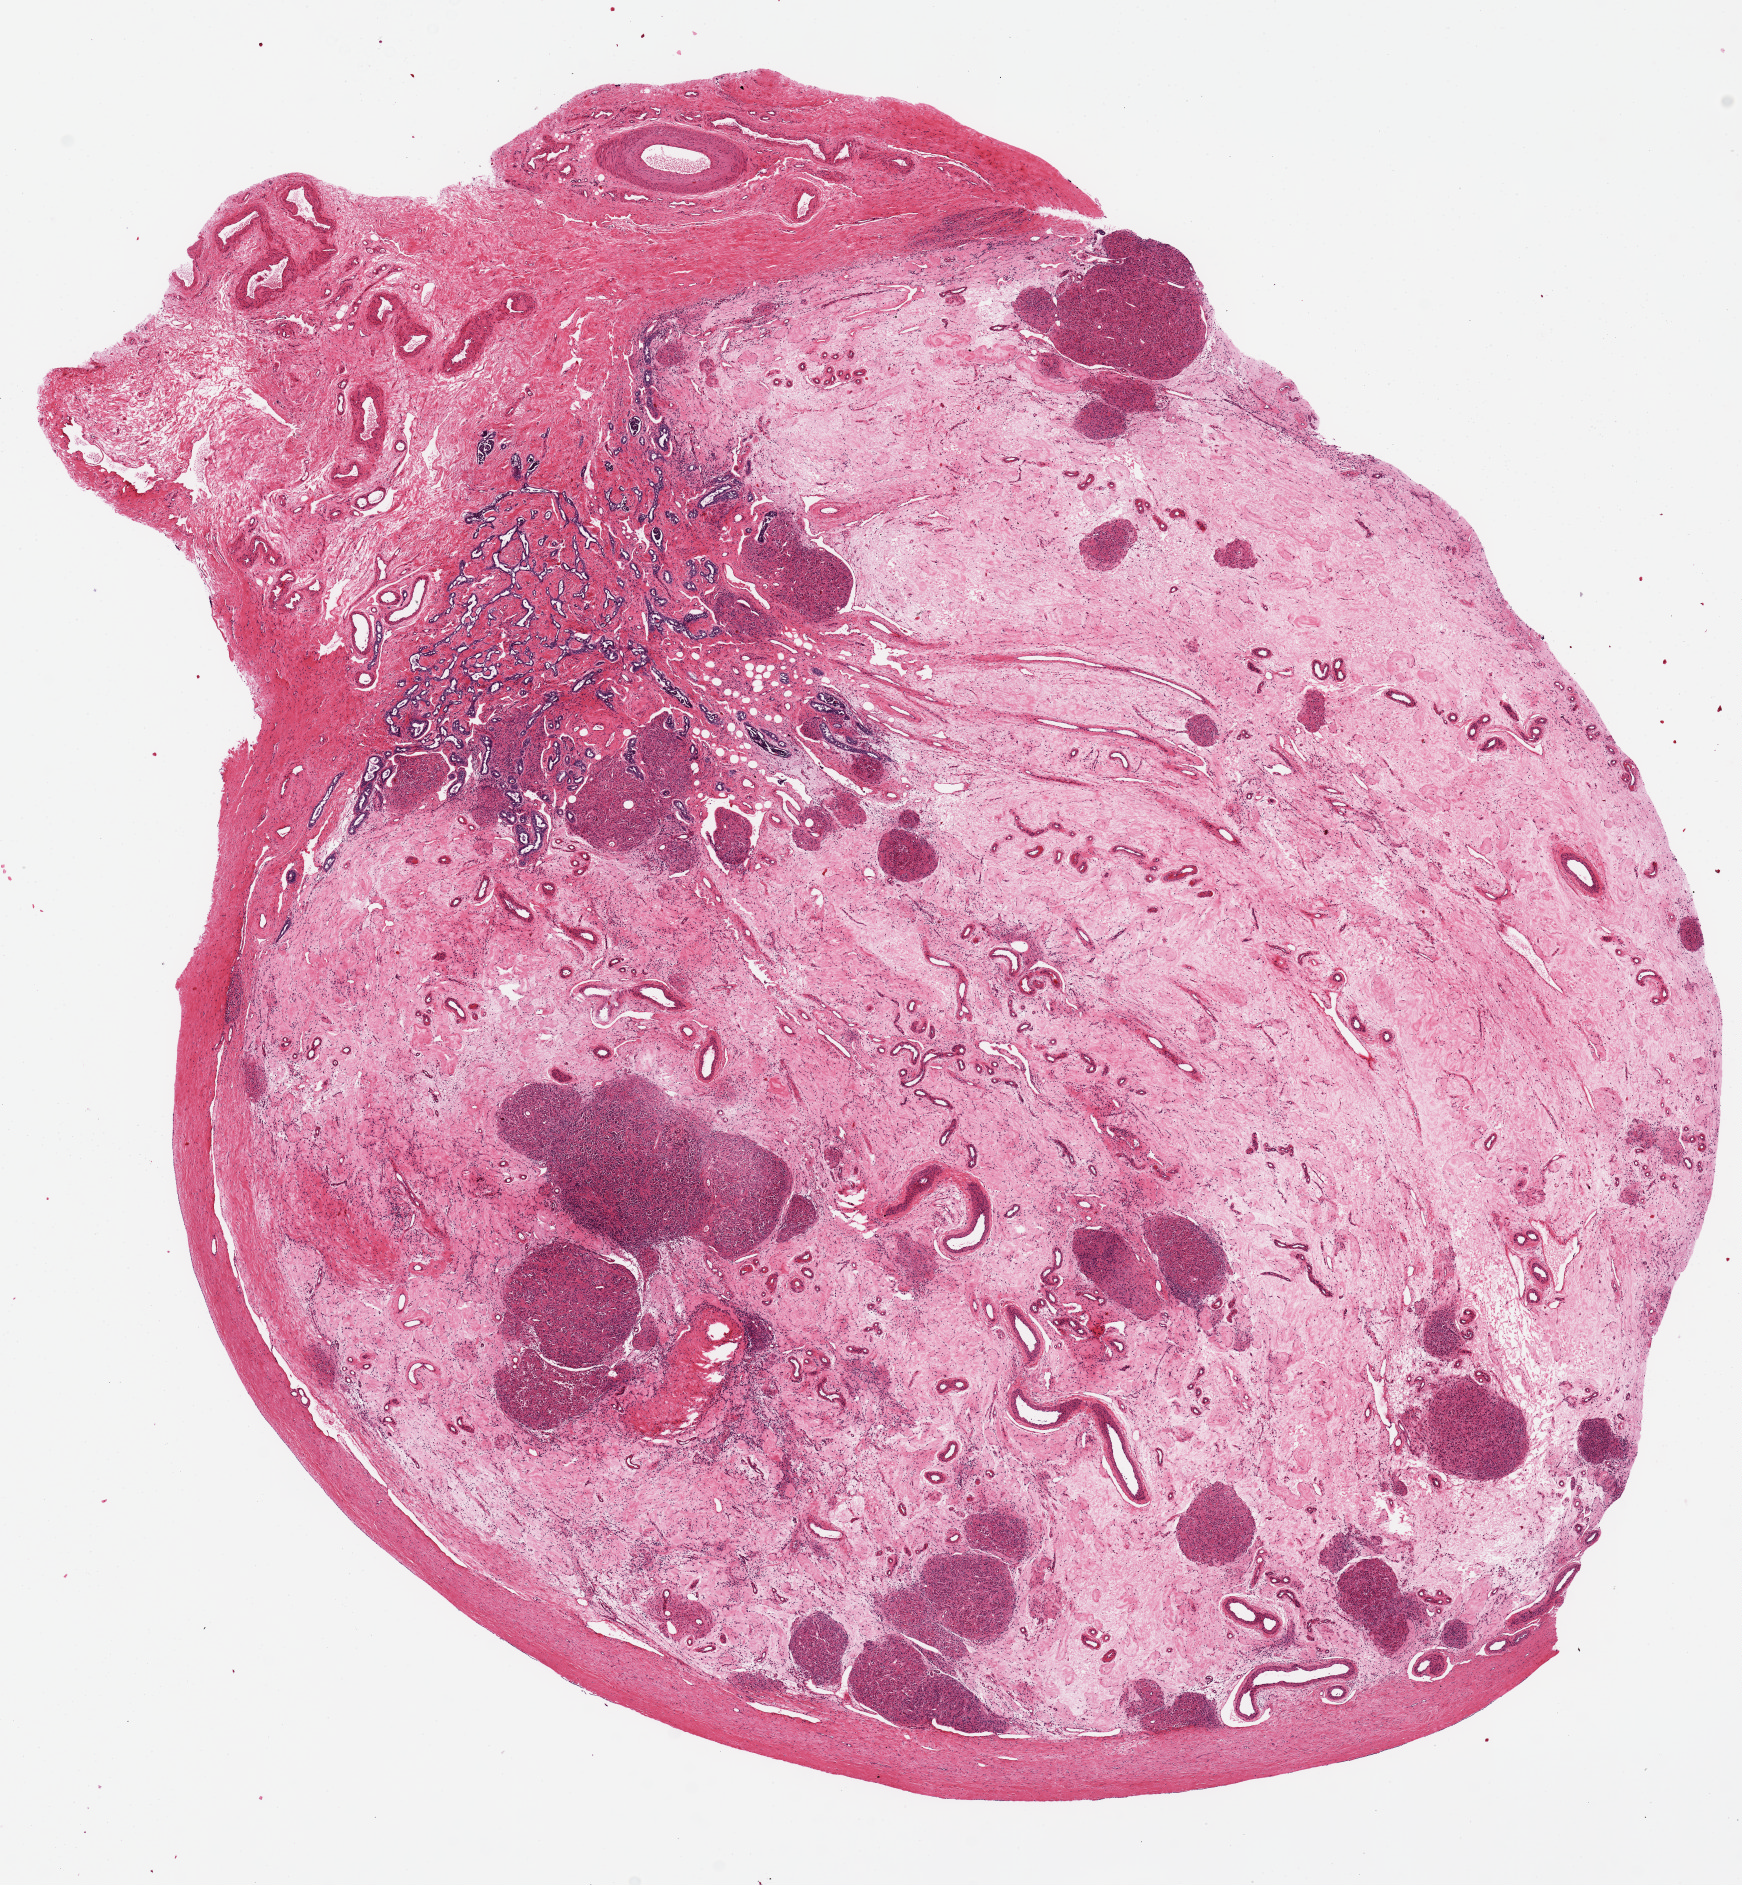
Digitized hematoxylin and eosin (H&E)-stained section, brightfield — whole scanned area (about 13.8 x 14.9 mm, slide scanned at 20x) shown as a low-resolution overview, PAXgene-fixed, paraffin-embedded tissue, section of testis (target tissue), tissue donor sample. Donor: male.
Reviewer comment on this tissue sample: Generalized atrophy of seminiferous tubules, nodular hyerplasia of Leydig cells. Rete testis is present.NA.